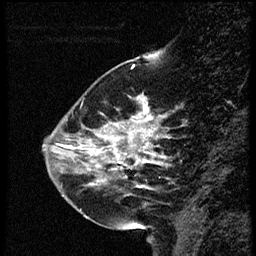
Breast MRI (dynamic contrast-enhanced), one sagittal slice; slice 15 of 56 in the series (ordered by position); dynamic contrast-enhanced study with each time point stored as its own series, time point 2 of 4 at this slice position (early post-contrast, ordered by acquisition time); 1.5 T; TE 4.2 ms, TR 18.9 ms; 256 × 256 image matrix, field of view 200 × 200 mm. Female patient. Case-level facts recorded for this patient, not image findings: setting: breast cancer imaged before/during neoadjuvant chemotherapy; receptor status: HER2-positive.
Structures marked on this image (semi-automatically segmented with operator editing):
- analysis volume of interest (the breast-tissue region the enhancement analysis was run in; not a lesion): bounding box [x1, y1, x2, y2] px = [63, 80, 169, 215]
- tumour enhancement mask (voxels above the 100 % enhancement threshold inside the analysis volume of interest): [90, 94, 159, 189]